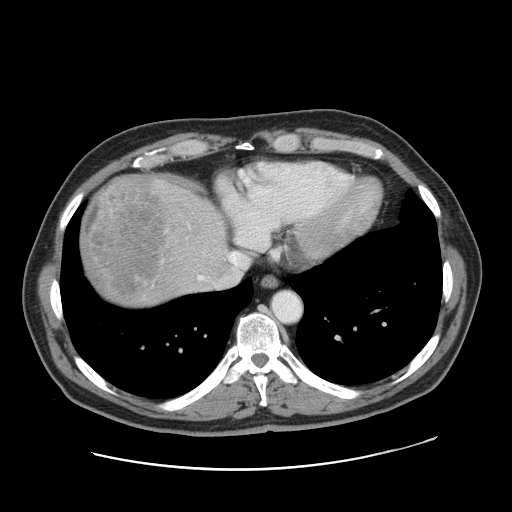
Contrast-enhanced abdominal CT, one axial slice; position 146 of 178 along the scan axis; intravenous contrast given; soft-tissue window (W 400 / L 40 HU); 2.5 mm slice thickness; 512 × 512 image matrix. Male patient, age 63 years. Case-level facts recorded for this patient, not image findings: diagnosis: colorectal cancer liver metastases, imaged before liver resection.
Structures marked on this image (expert manual segmentation):
- hepatic veins: bounding box (x1, y1, x2, y2) in pixels: (199, 252, 249, 287)
- liver: (80, 175, 228, 308)
- planned liver remnant (the part of the liver to remain after resection): (184, 190, 228, 262)
- liver metastasis: (83, 177, 165, 295)